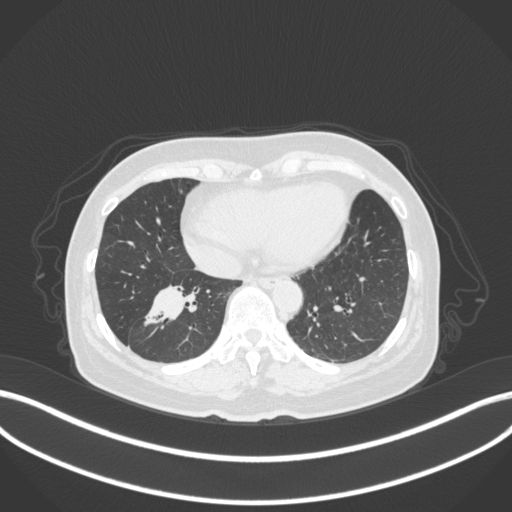
Chest CT, one axial slice. Position 128 of 429 along the scan axis. 120 kVp. Lung window (W 1500 / L -600 HU). 512 × 512 image matrix, field of view 400 × 400 mm. Patient: female, 67 years. Case-level facts recorded for this patient, not image findings: clinical TNM (as recorded): T1c N1 M0.
Structures marked on this image (bounding box drawn by a radiologist):
- lung tumour (recorded histology: adenocarcinoma): bounding box (x1, y1, x2, y2) in pixels: (140, 283, 204, 333)